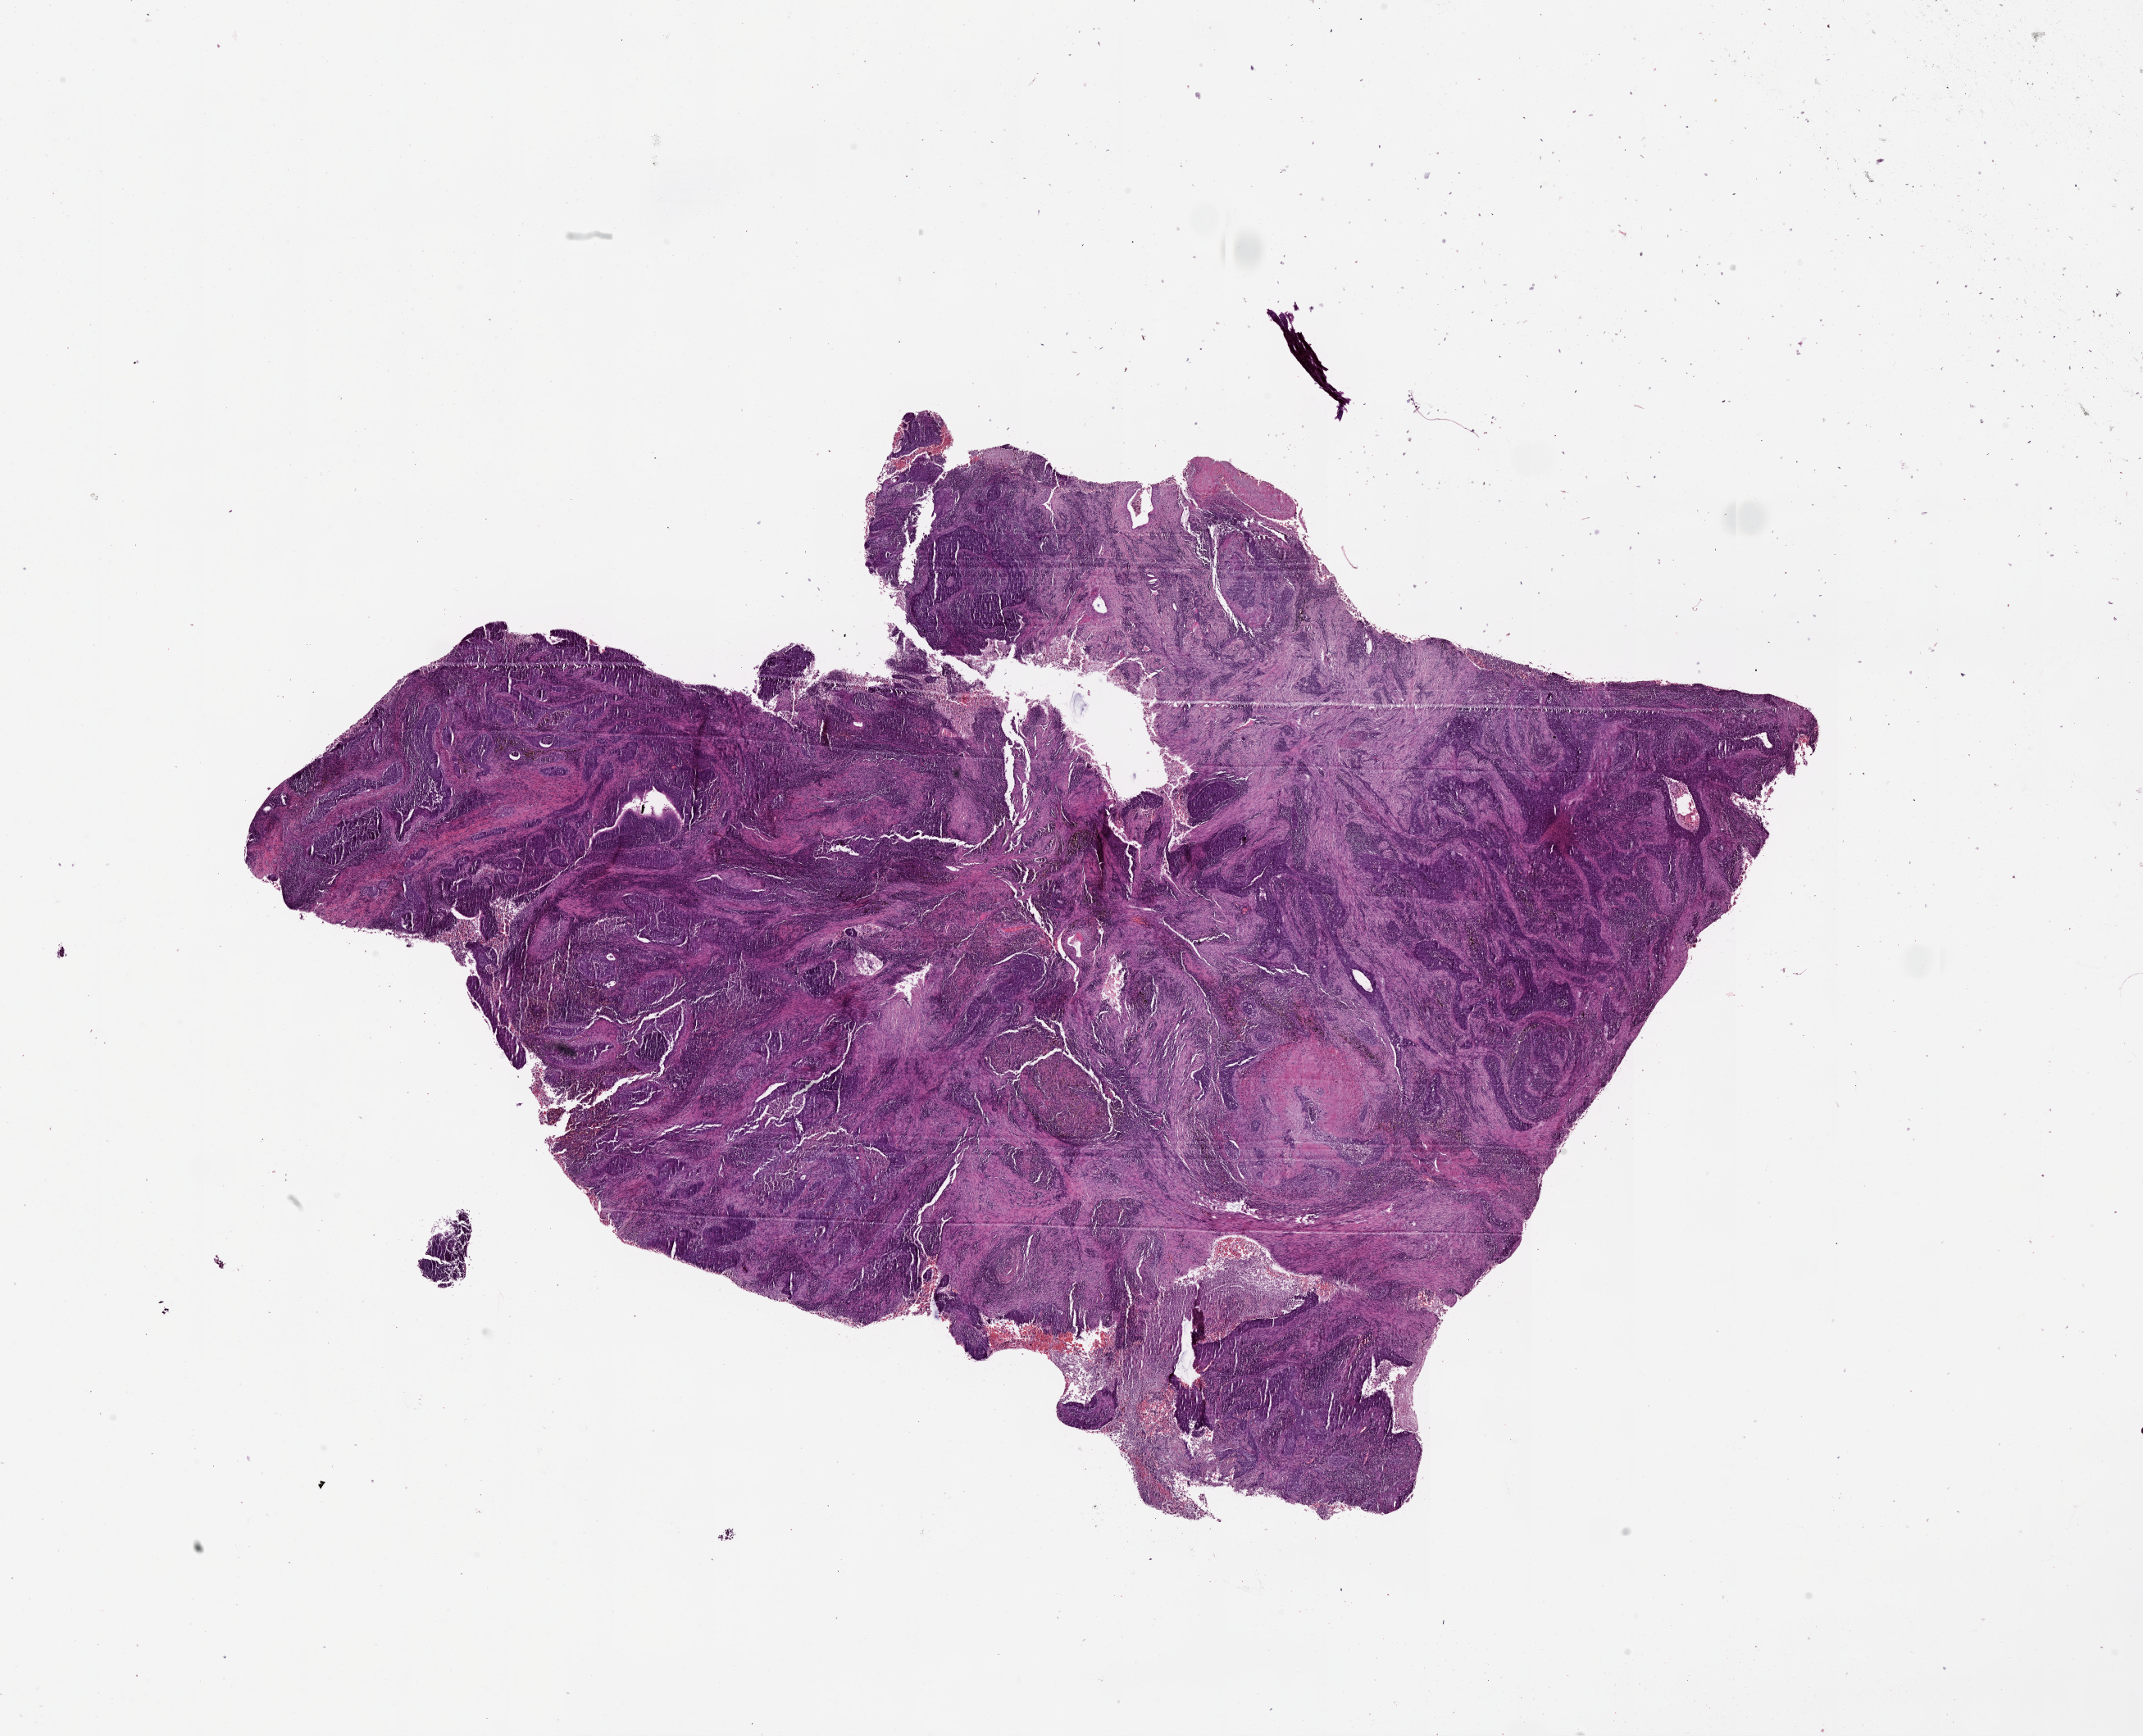
Digitized H&E tissue section (whole slide), whole scanned area (about 21.0 x 17.1 mm) shown as a low-resolution overview, tumour tissue sample, lung. Patient: male, age 59 years.
* patient diagnosis (cohort enrolment): squamous cell carcinoma (lung)